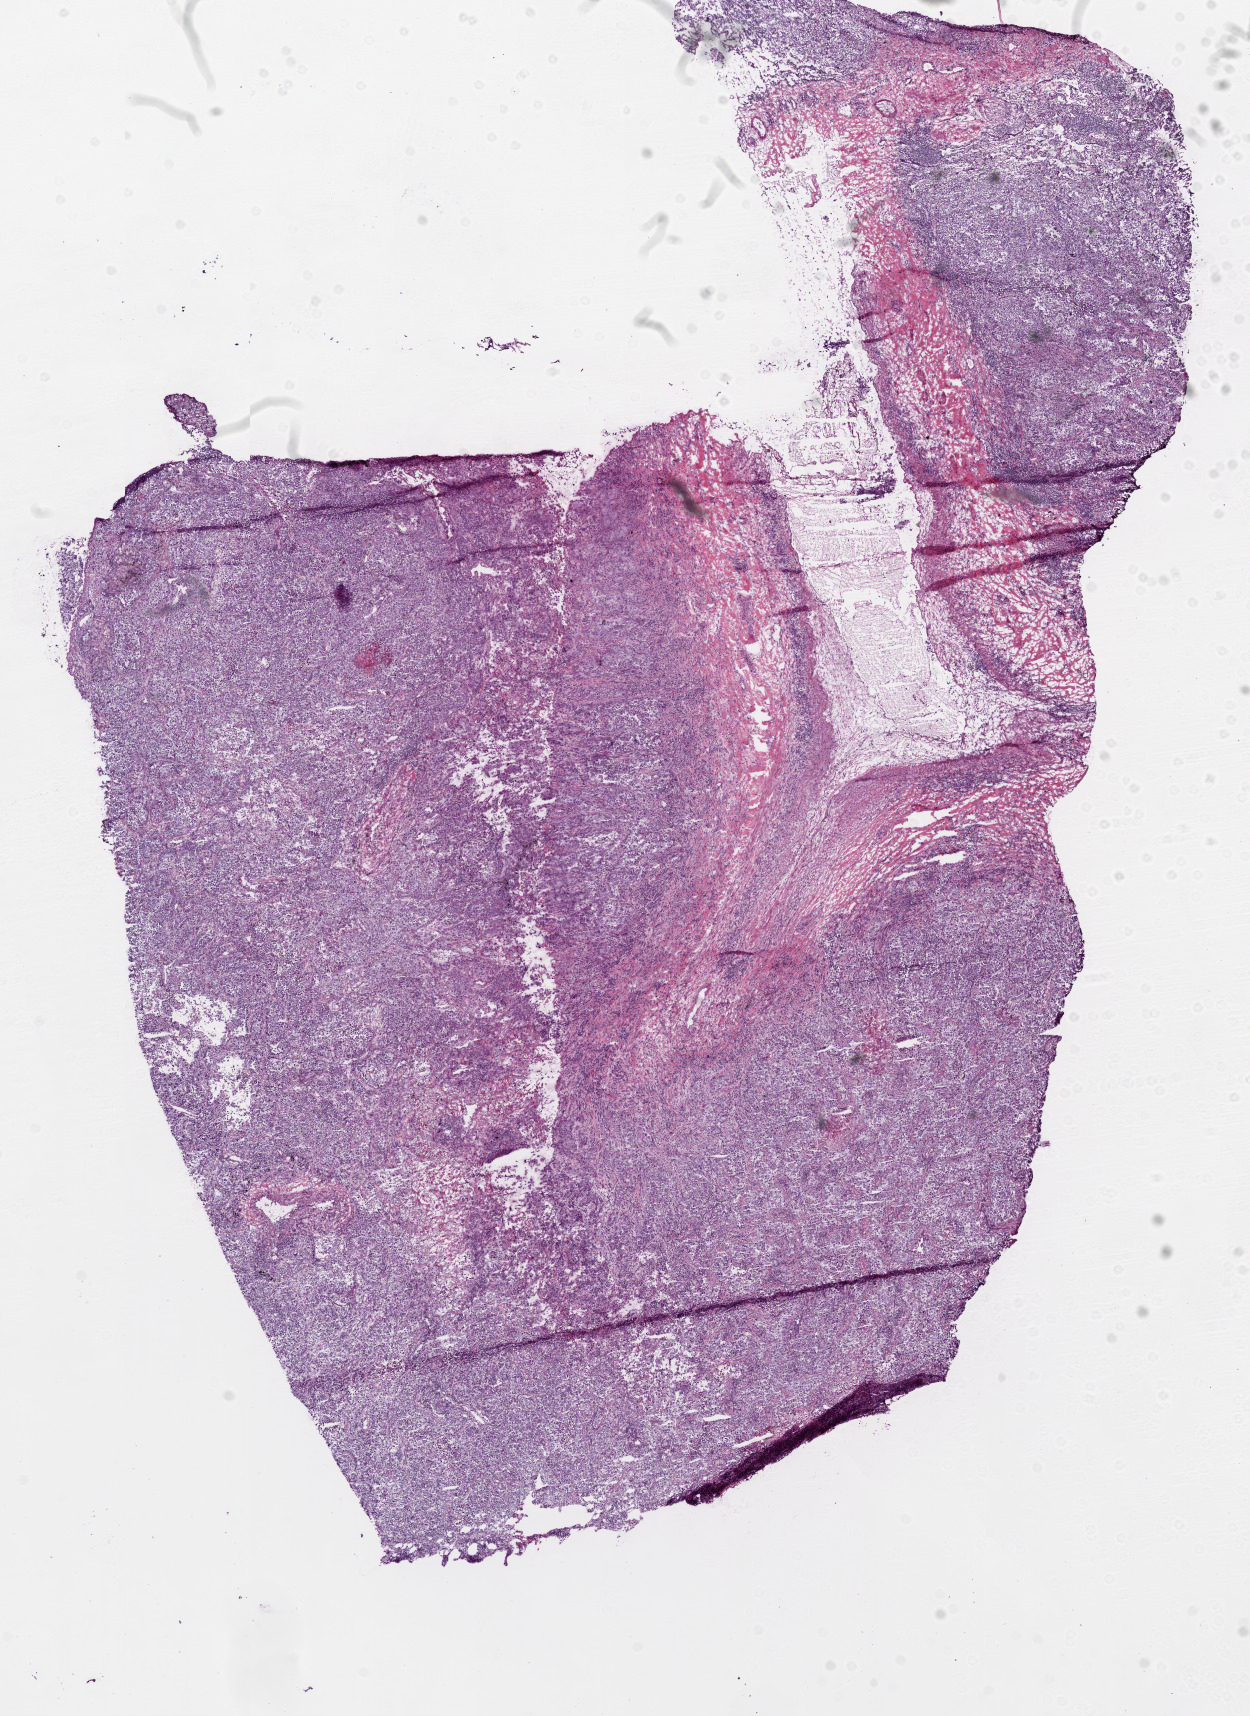
Digitized H&E tissue section (whole slide) — shown as a low-resolution overview of the whole scanned area (about 10.0 x 13.8 mm, slide scanned at 20x), frozen section from the bottom of the tissue portion, sample: primary tumour, lung. Female patient; age at initial diagnosis 47 years. Slide review estimates, as recorded: tumour nuclei 70%, normal cells 0%, stromal cells 10%, necrosis 5%.
Laterality: right. Pathologic diagnosis: Adenocarcinoma with mixed subtypes (upper lobe, lung). AJCC pathologic stage: IIIB (5th edition).